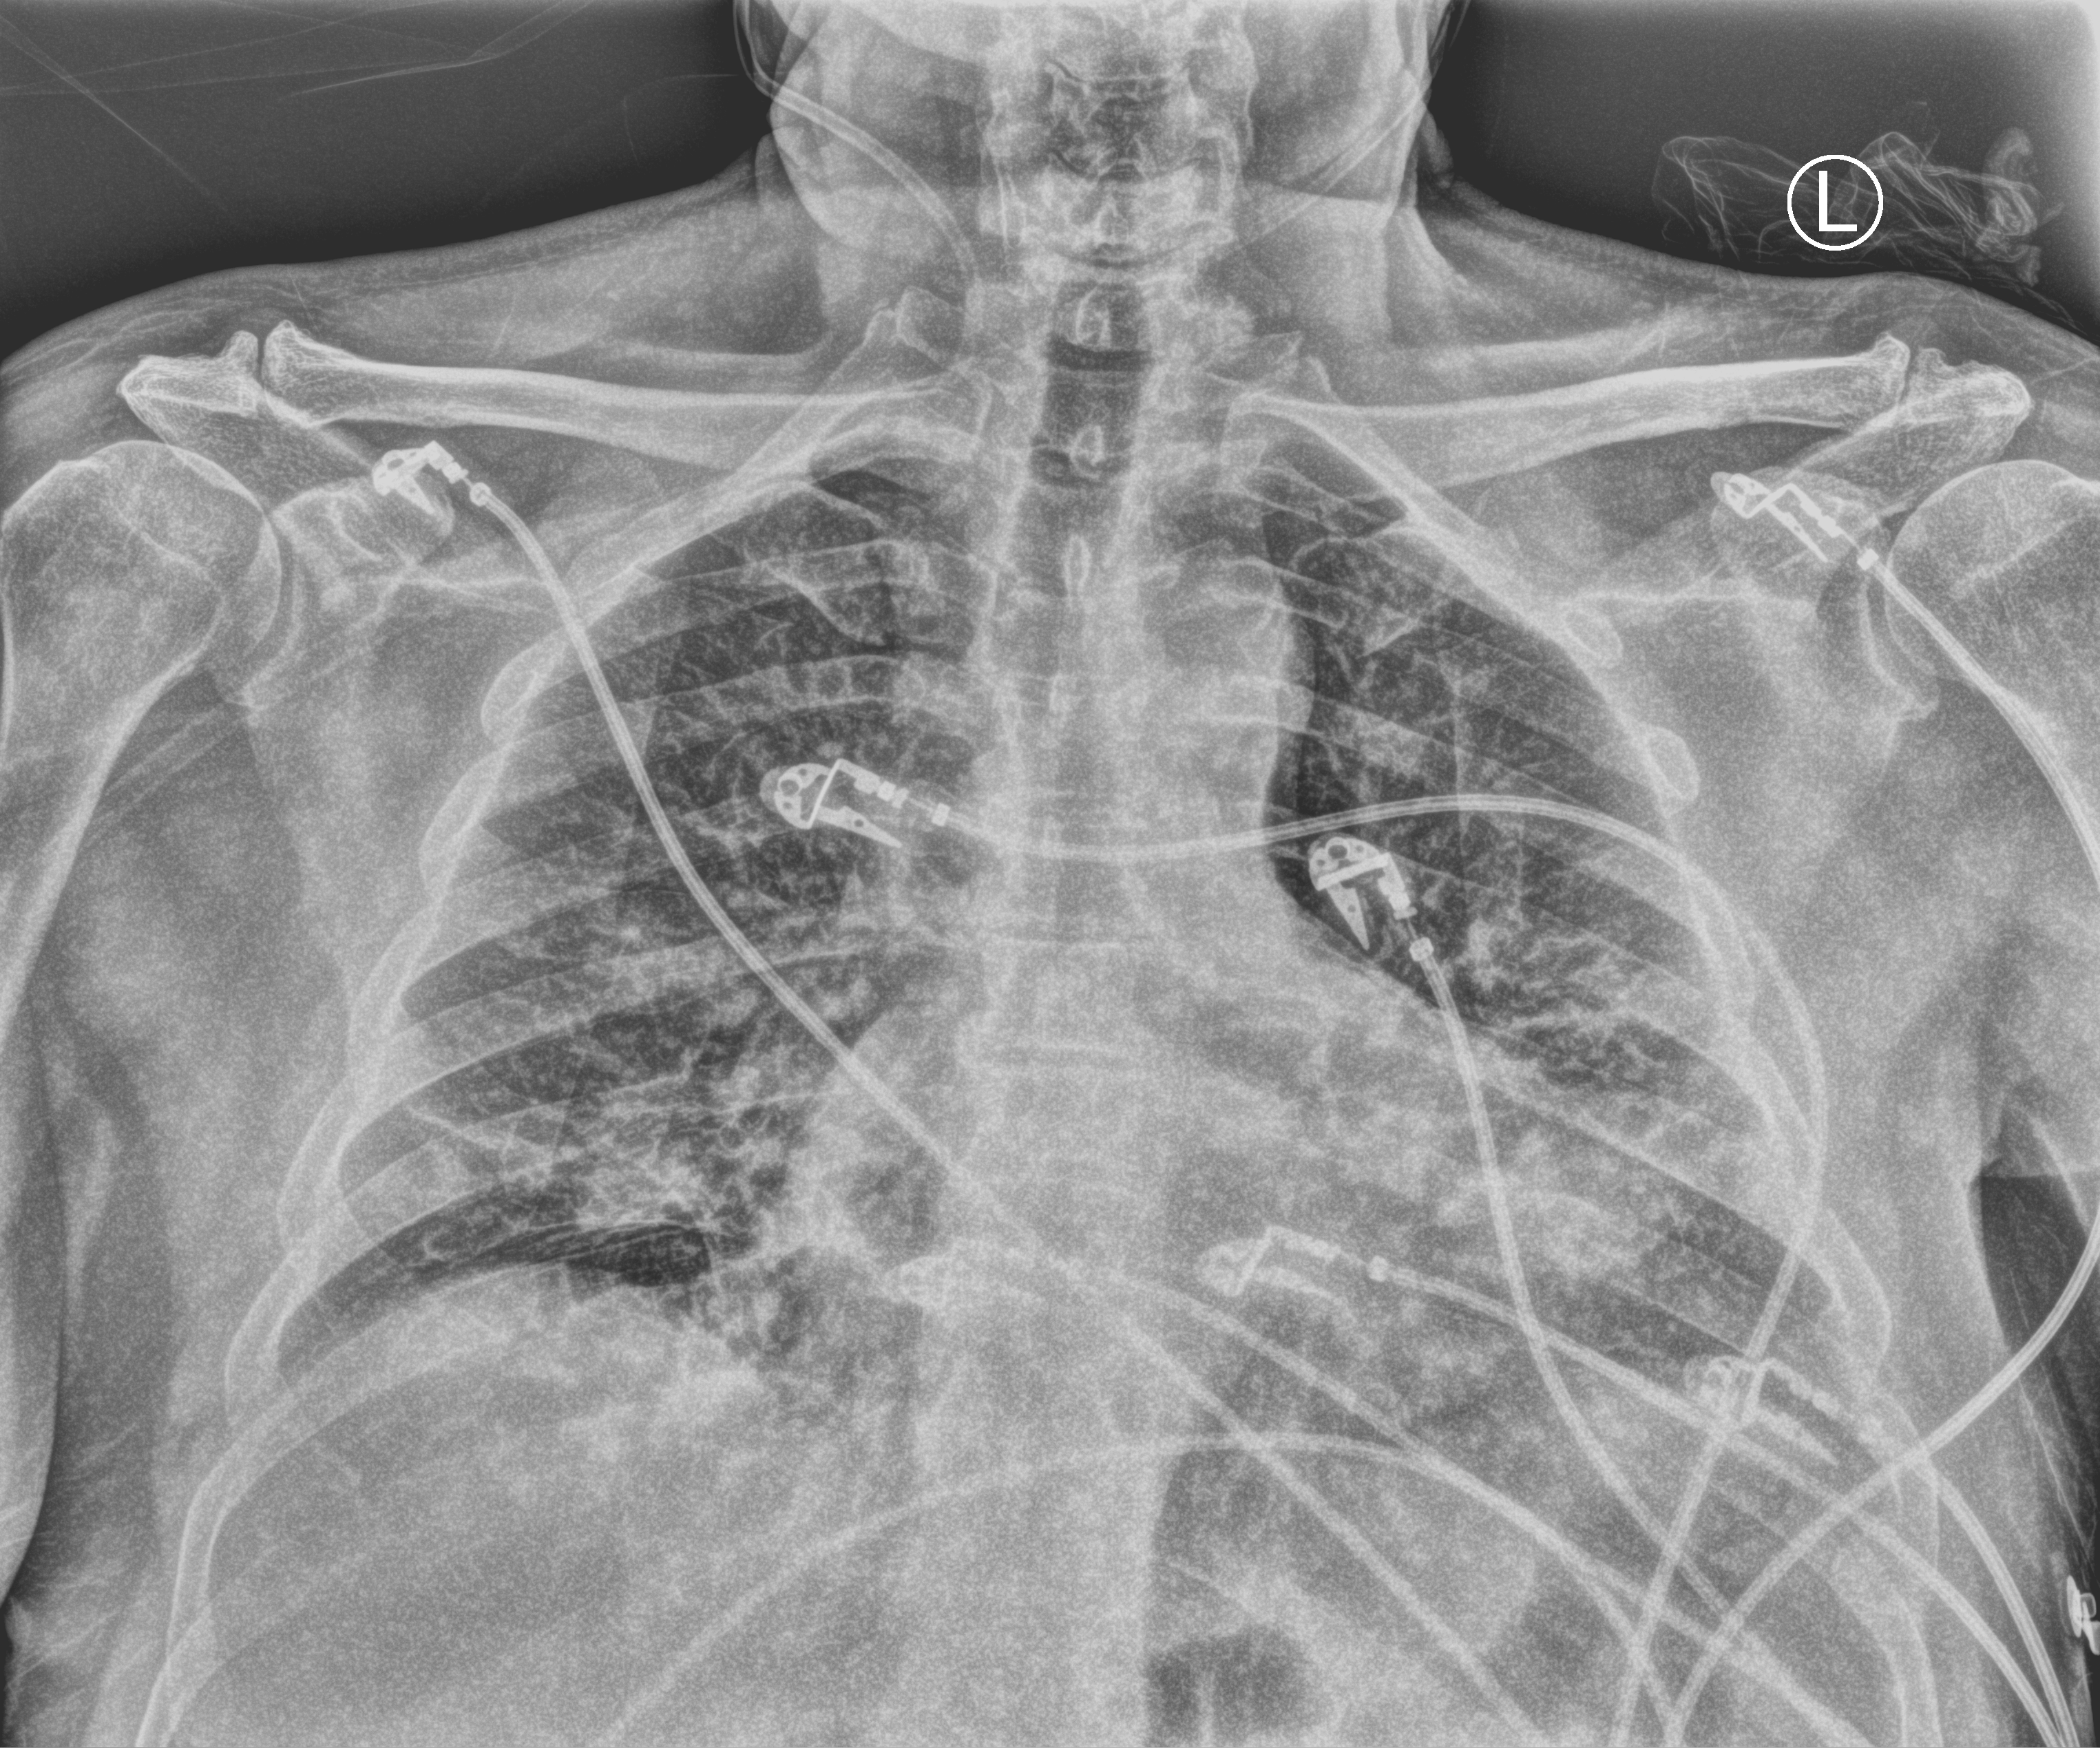
Chest X-ray (portable); anteroposterior (AP) projection. Male patient hospitalised with COVID-19, age 60–74 years.
Hospital-stay facts (about this admission, not read from this image; timing relative to this image not recorded): COPD (admission record): no; length of hospital stay: 20 days; chronic kidney disease (admission record): no.